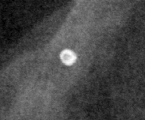
Crop from a digitized film mammogram around one marked abnormality, right breast, CC view.
Finding: calcifications, morphology coarse; BI-RADS assessment category 2; subtlety rating 4 on a 1 (subtle) to 5 (obvious) scale; benign; no additional work-up was recommended (benign without callback).